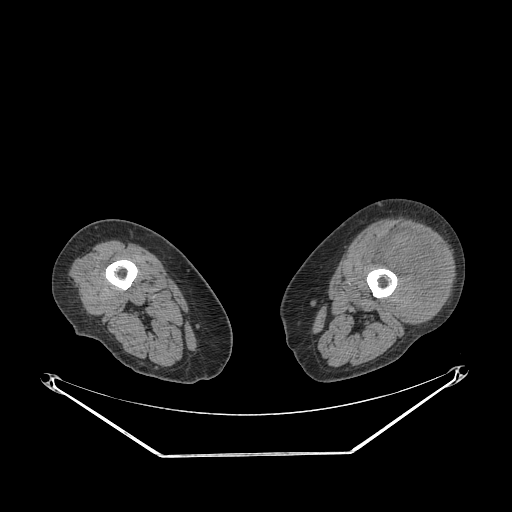
CT of an extremity soft-tissue mass (from a PET/CT study), one axial slice; position 210 of 267 along the scan axis; reconstruction kernel STANDARD; 140 kVp; soft-tissue window (W 400 / L 40 HU); 3.75 mm slice thickness; 512 × 512 image matrix, field of view 500 × 500 mm. Female patient. From the clinical record (not read from this slice): histological type: undifferentiated – high grade; grade: high; site of the primary tumour: left thigh.
Structures marked on this image (expert contour drawn on MRI and transferred to this co-registered scan by the dataset authors):
- gross tumour volume including surrounding oedema: bounding box <365,231,448,320> (left, top, right, bottom; pixels)
- gross tumour volume (mass): <377,231,446,320>